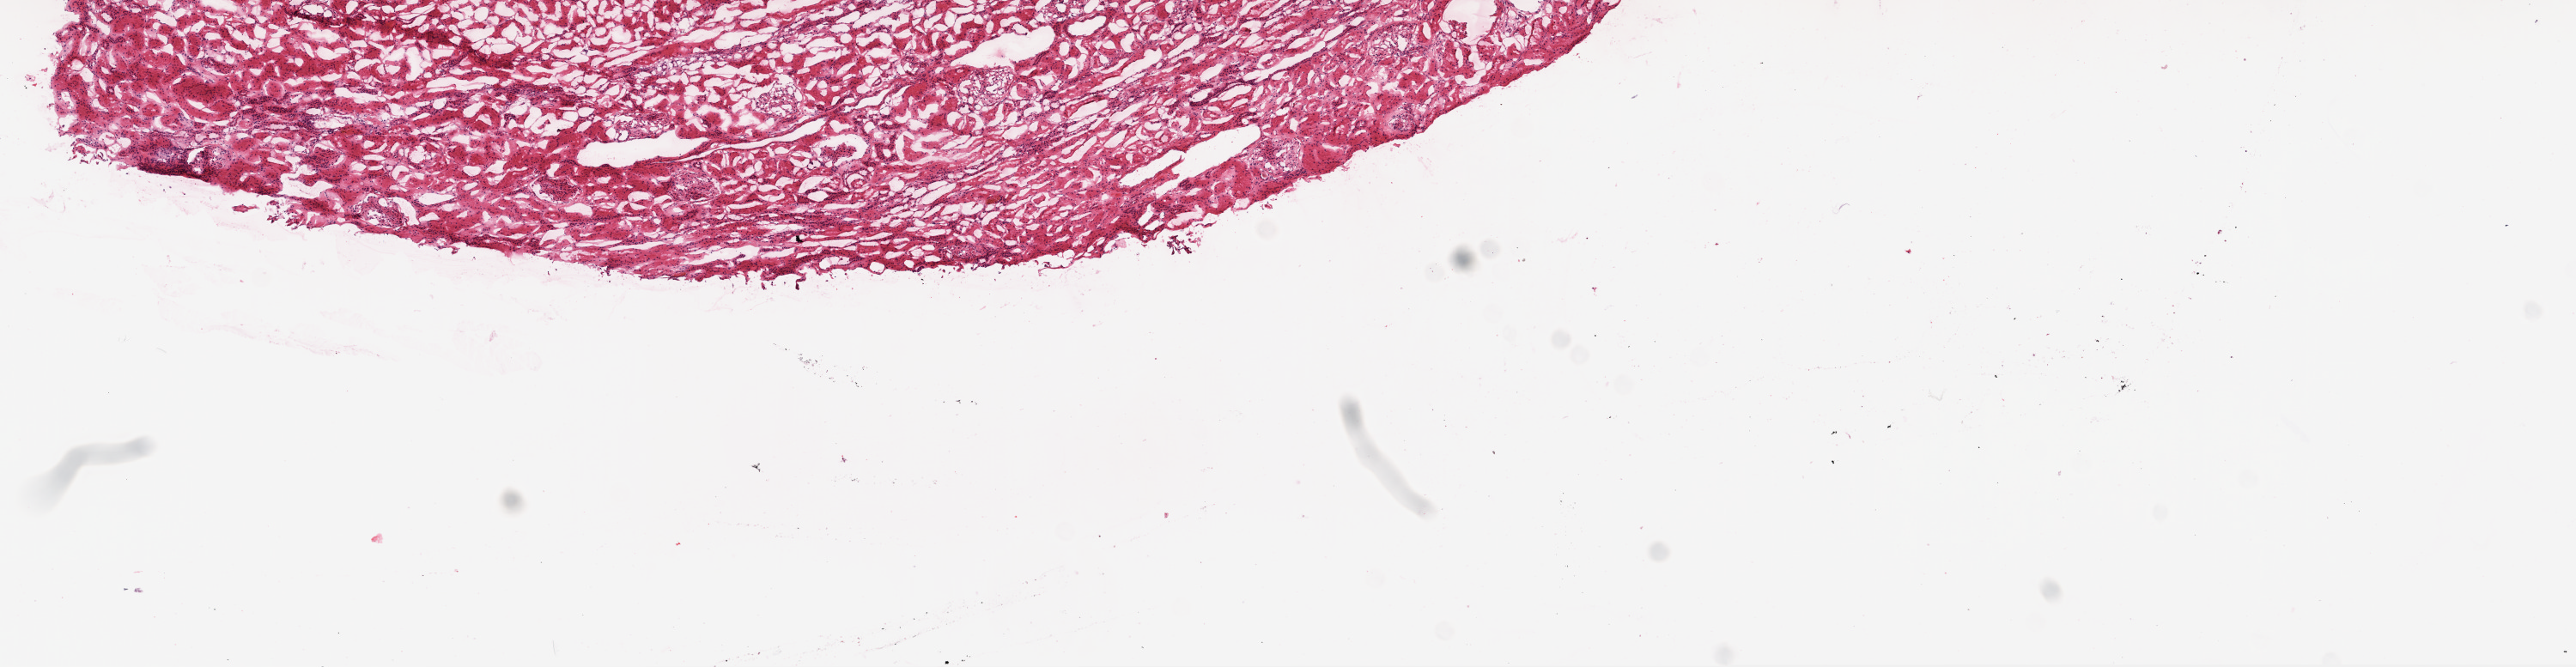
Whole-slide histology image, Hematoxylin and eosin (H&E) stained, low-resolution overview of the scanned area, about 12.0 x 3.1 mm (from a 20x scan), frozen section from the top of the tissue portion, sample: solid tissue normal (non-tumour tissue), kidney. Patient: male, age at initial diagnosis 54 years.
This section: solid tissue normal sample (biorepository sample class). Patient diagnosis: Clear cell adenocarcinoma, NOS.